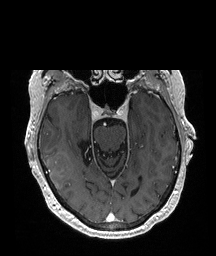
Brain MRI from a brain-tumour surgery series, one axial slice. Slice 134 of 208 in the series (ordered by position). T1-weighted post-contrast. 1 mm slice thickness. 216 × 256 image matrix, field of view 216 × 256 mm. Case-level facts recorded for this patient, not image findings: histopathology: Glioblastoma; WHO grade: 4; IDH mutation: no.
Structures marked on this image (outlined manually by an expert reader):
- tumour: box from (x=44, y=152) to (x=73, y=189) px